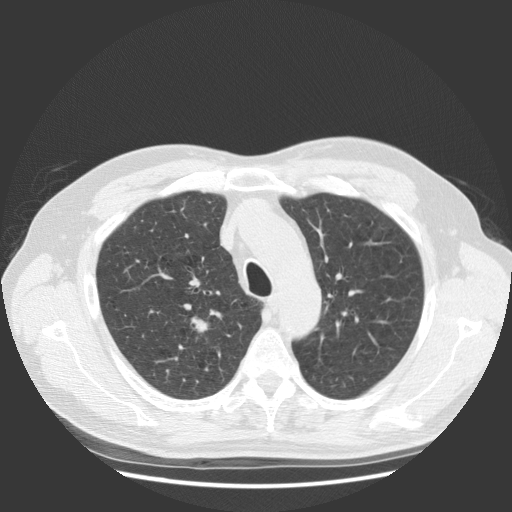
Low-dose screening chest CT, one axial slice. Slice 96 of 131 in the series (ordered by position). Reconstruction kernel STANDARD. 140 kVp. Lung window (W 1500 / L -600 HU). 2.5 mm slice thickness. 512 × 512 image matrix, field of view 369 × 369 mm.
Outlined on this slice (outlined manually by an expert reader):
- lesion 1 (tumor, upper lobe of right lung): bounding box <191,317,208,332> (left, top, right, bottom; pixels)